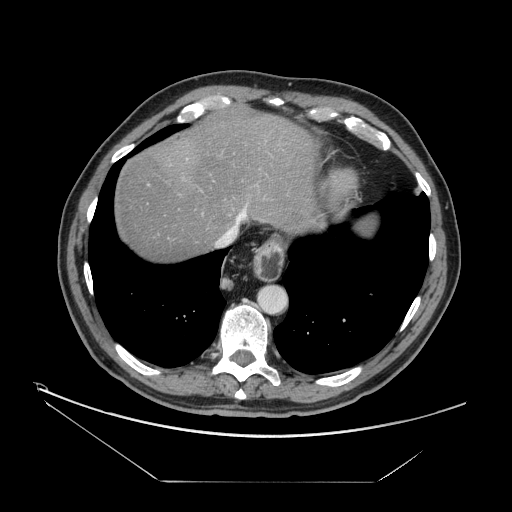
Contrast-enhanced abdominal CT, one axial slice. Slice 138 of 161 in the series (ordered by position). Reconstruction kernel STANDARD. 120 kVp. Soft-tissue window (W 400 / L 40 HU). 512 × 512 image matrix, field of view 440 × 440 mm. Male patient, age 65 years. Case-level facts recorded for this patient, not image findings: diagnosis: colorectal cancer liver metastases, imaged before liver resection; multiple liver metastases: yes; largest metastasis: 4.2 cm; disease in both lobes: yes.
Annotated regions visible in this slice (expert manual segmentation):
- hepatic veins: bounding box (x1, y1, x2, y2) in pixels: (219, 205, 248, 244)
- liver: (114, 108, 317, 260)
- planned liver remnant (the part of the liver to remain after resection): (114, 108, 316, 260)